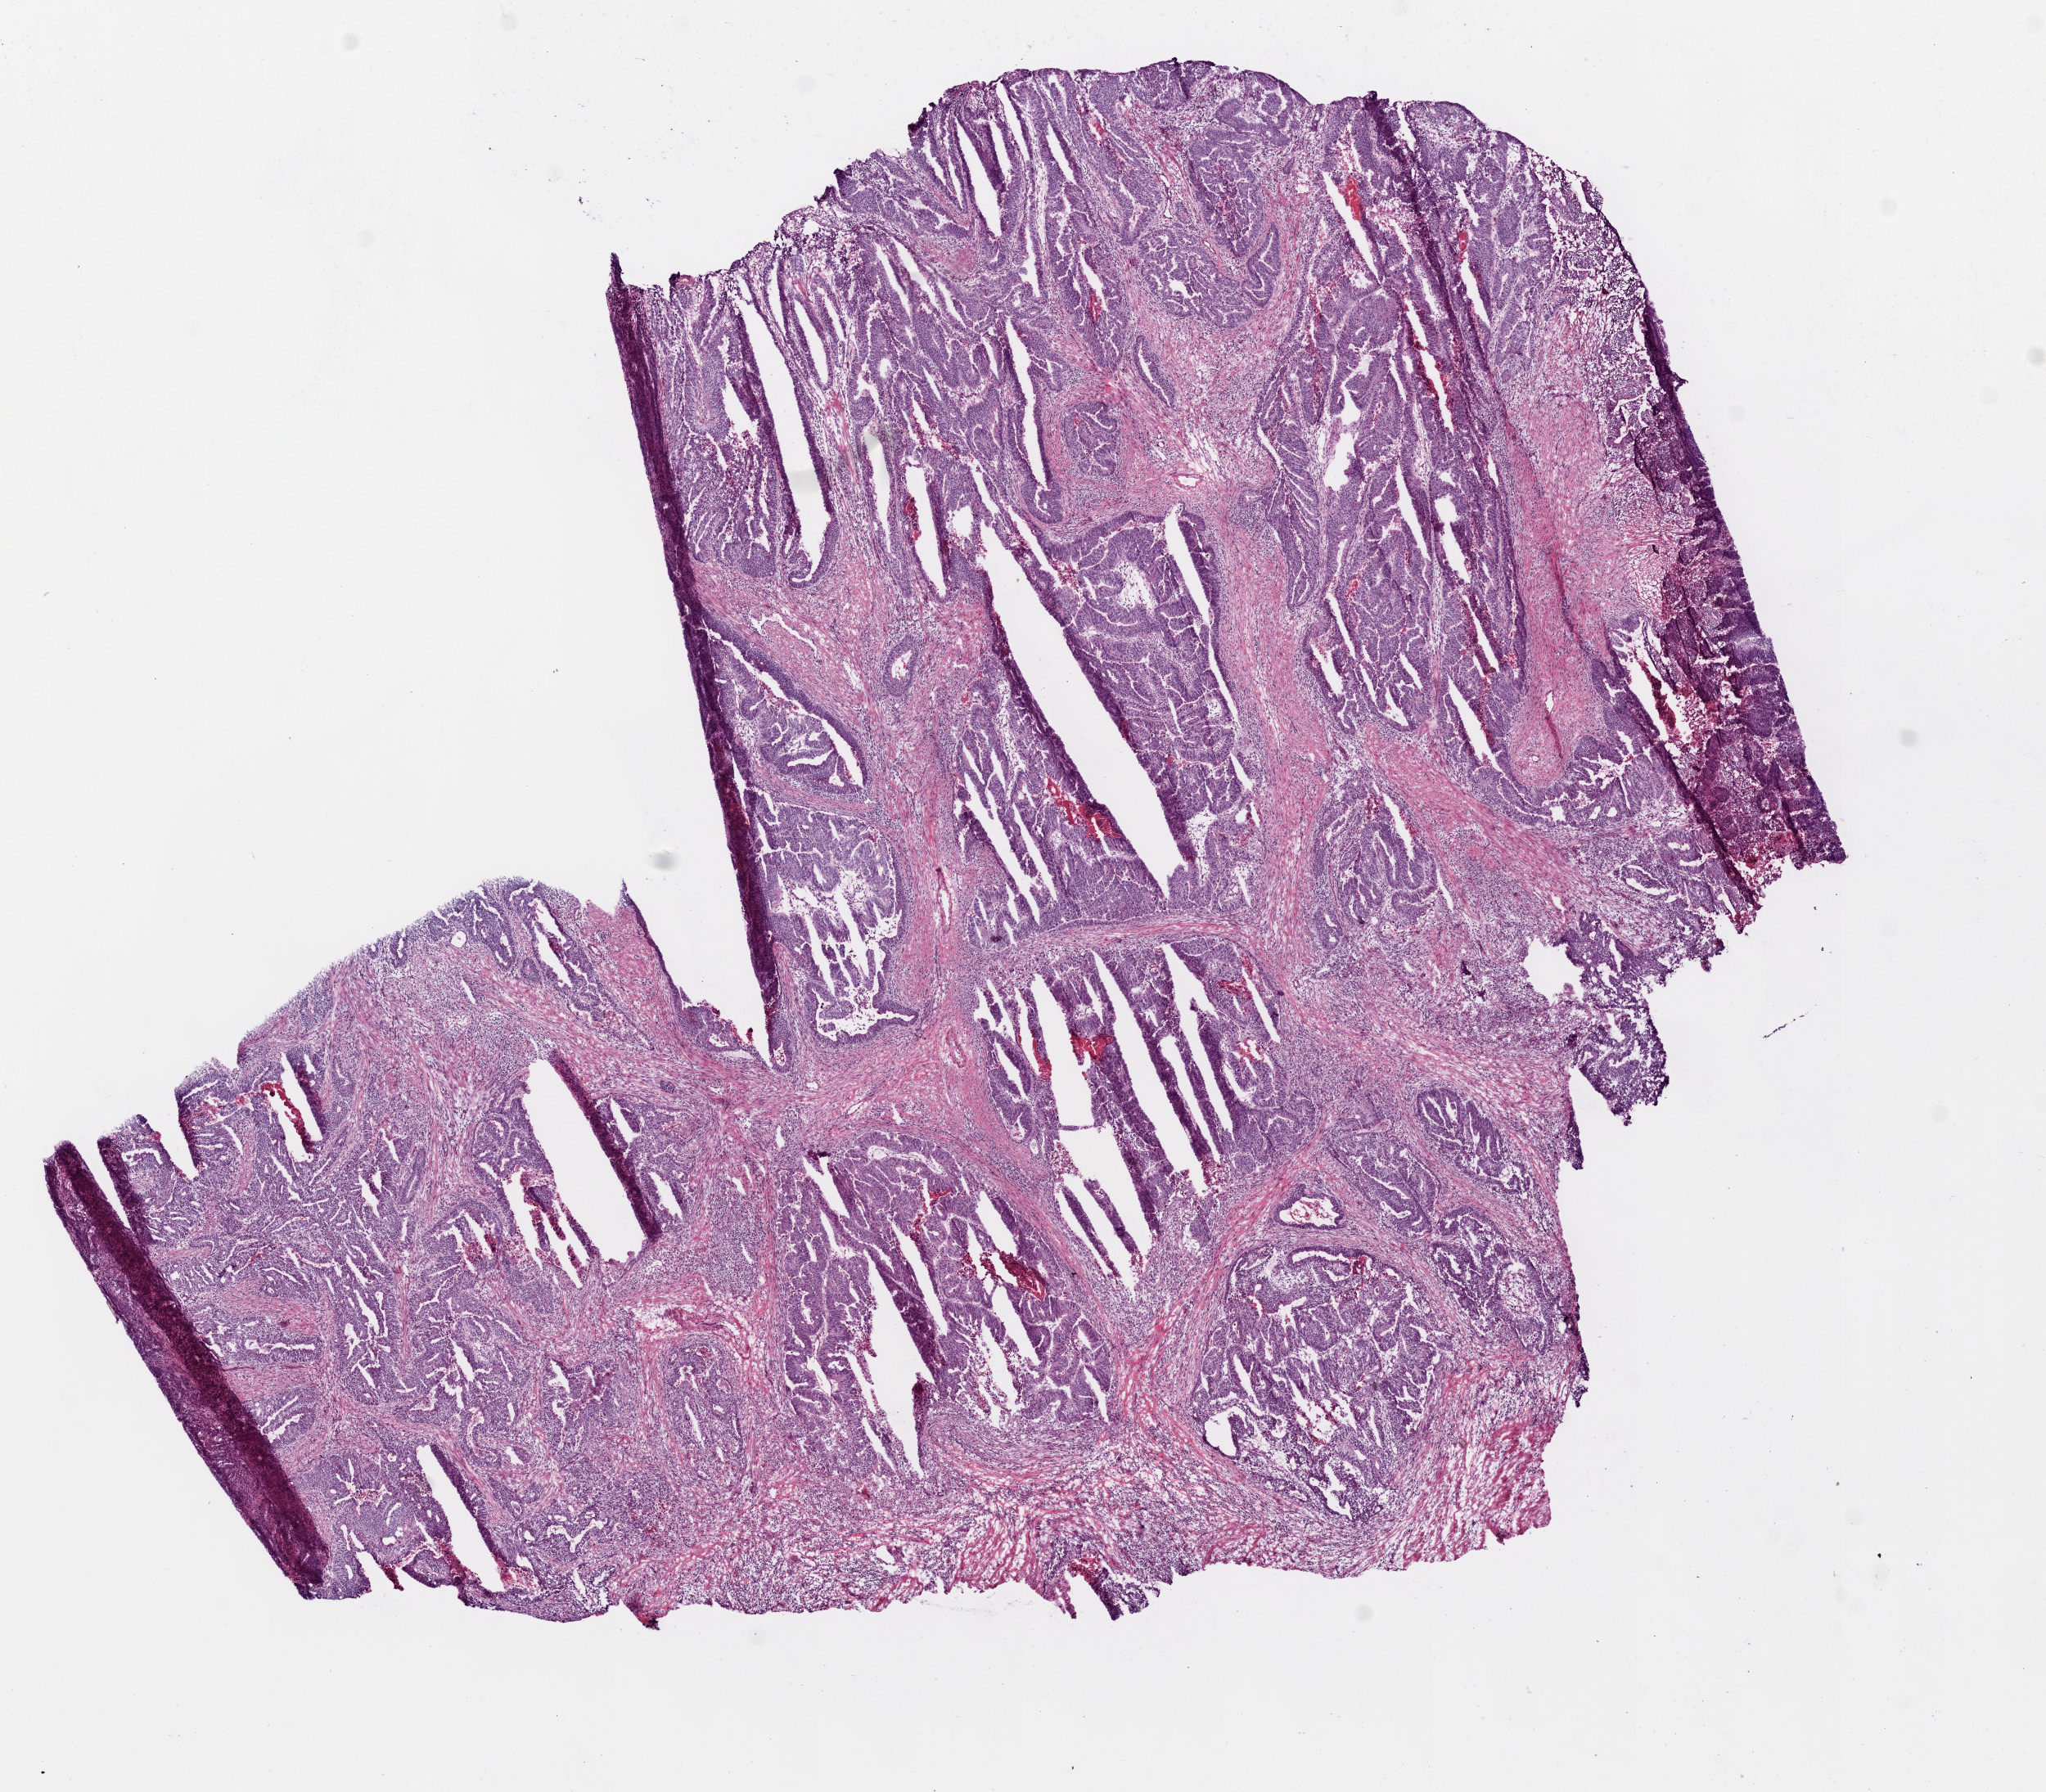
Whole-slide histology image, H&E-stained, whole scanned area (about 10.0 x 8.8 mm, slide scanned at 20x) shown as a low-resolution overview. Frozen section. Primary tumour sample from the rectum. Female patient; age at initial diagnosis 55 years. Pathologist review of this section (percent, as recorded): tumour cells 80%, tumour nuclei 88%, normal cells 10%, stromal cells 8%, necrosis 2%.
* histologic diagnosis: Adenocarcinoma, NOS
* AJCC pathologic stage: IIIB (6th edition)